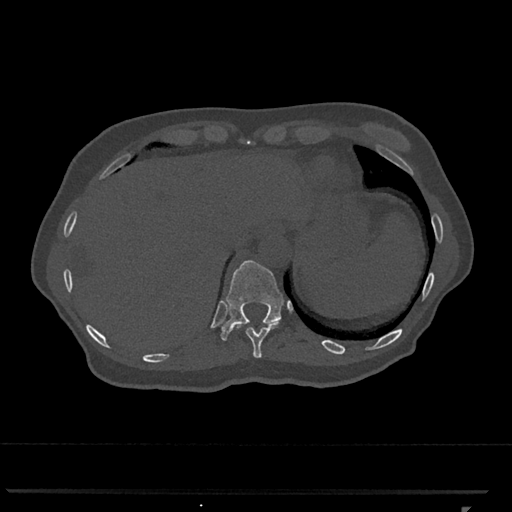
CT including the spine, one axial slice; position 540 of 793 along the scan axis; reconstruction kernel Br40s/3; bone window (W 1800 / L 400 HU); 512 × 512 image matrix, field of view 380 × 380 mm. Female patient, age 62 years. From the clinical record (not read from this slice): primary cancer: renal.
Outlined on this slice (semi-automatic segmentation, software-assisted and operator-edited):
- T10 vertebra: bounding box [x1, y1, x2, y2] px = [237, 322, 278, 358]
- T11 vertebra: [220, 260, 284, 341]